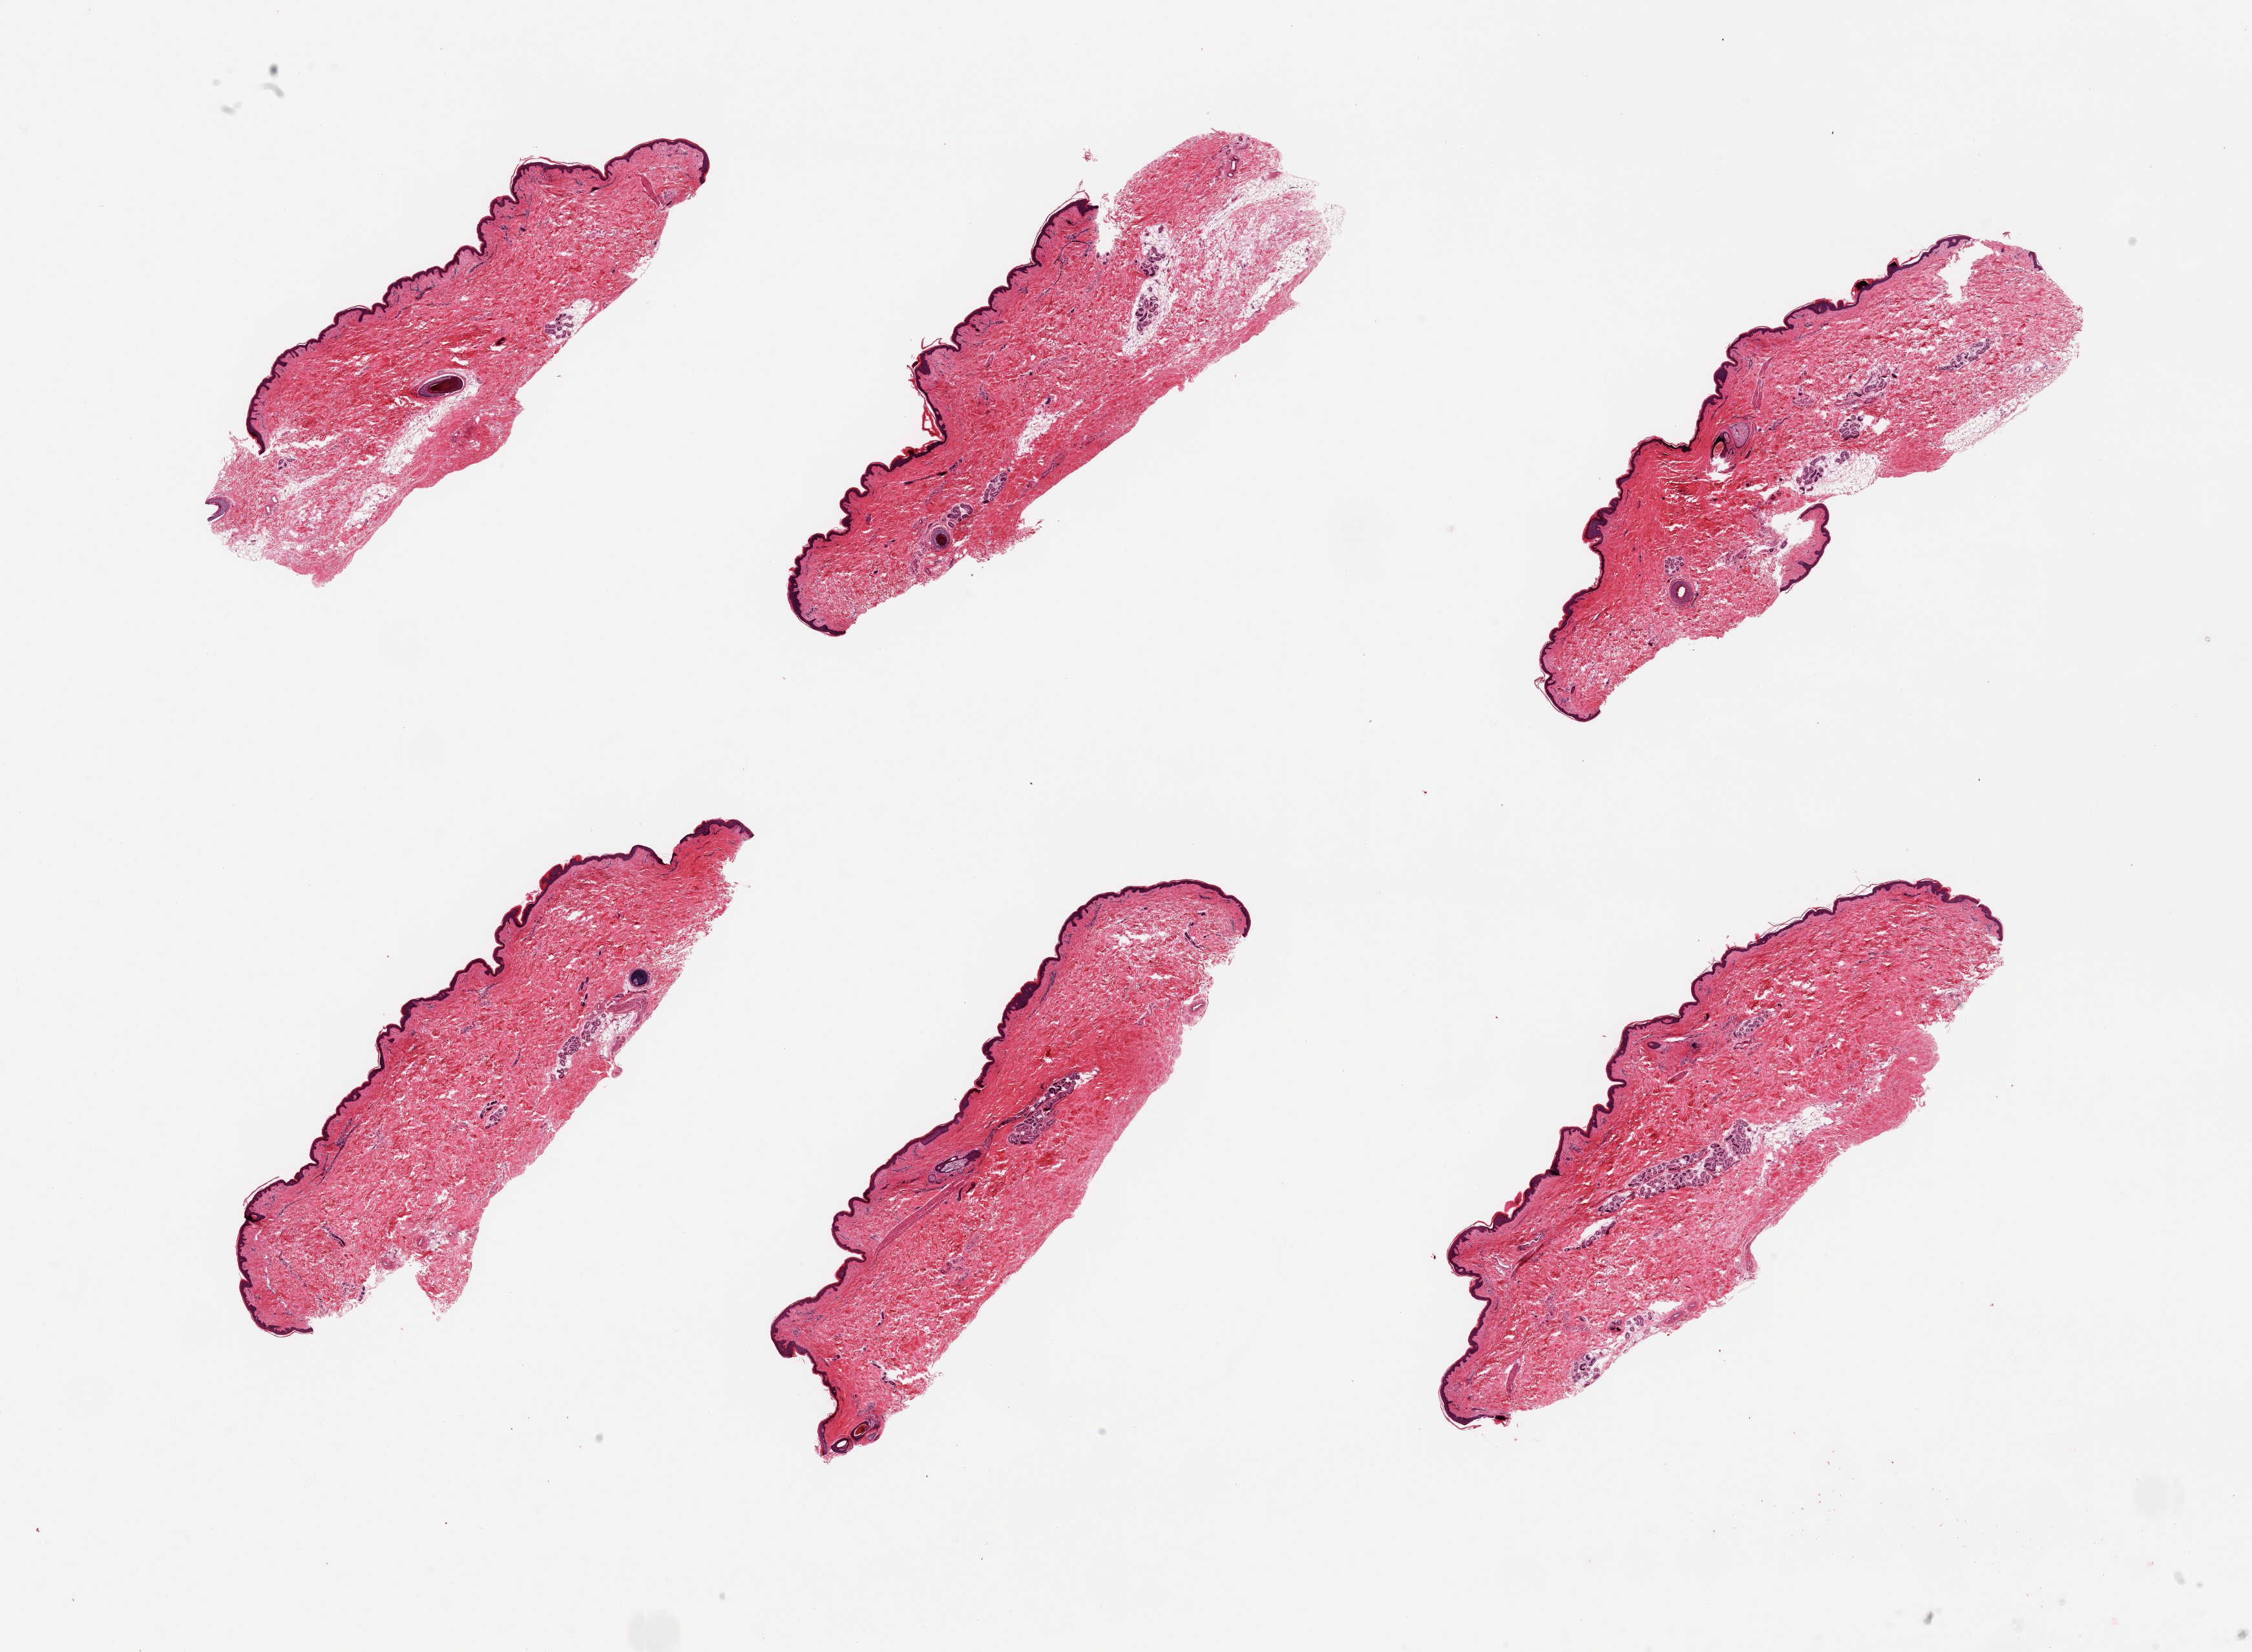
Whole-slide image, H&E stain — shown as a low-resolution overview of the whole scanned area (about 27.6 x 20.2 mm, slide scanned at 20x). PAXgene-fixed, paraffin-embedded tissue. Sampled site (target tissue): skin of suprapubic region. Tissue donor sample. Male donor.
Review note (as recorded): 6 pieces; well trimmed; 10% dermal fat.